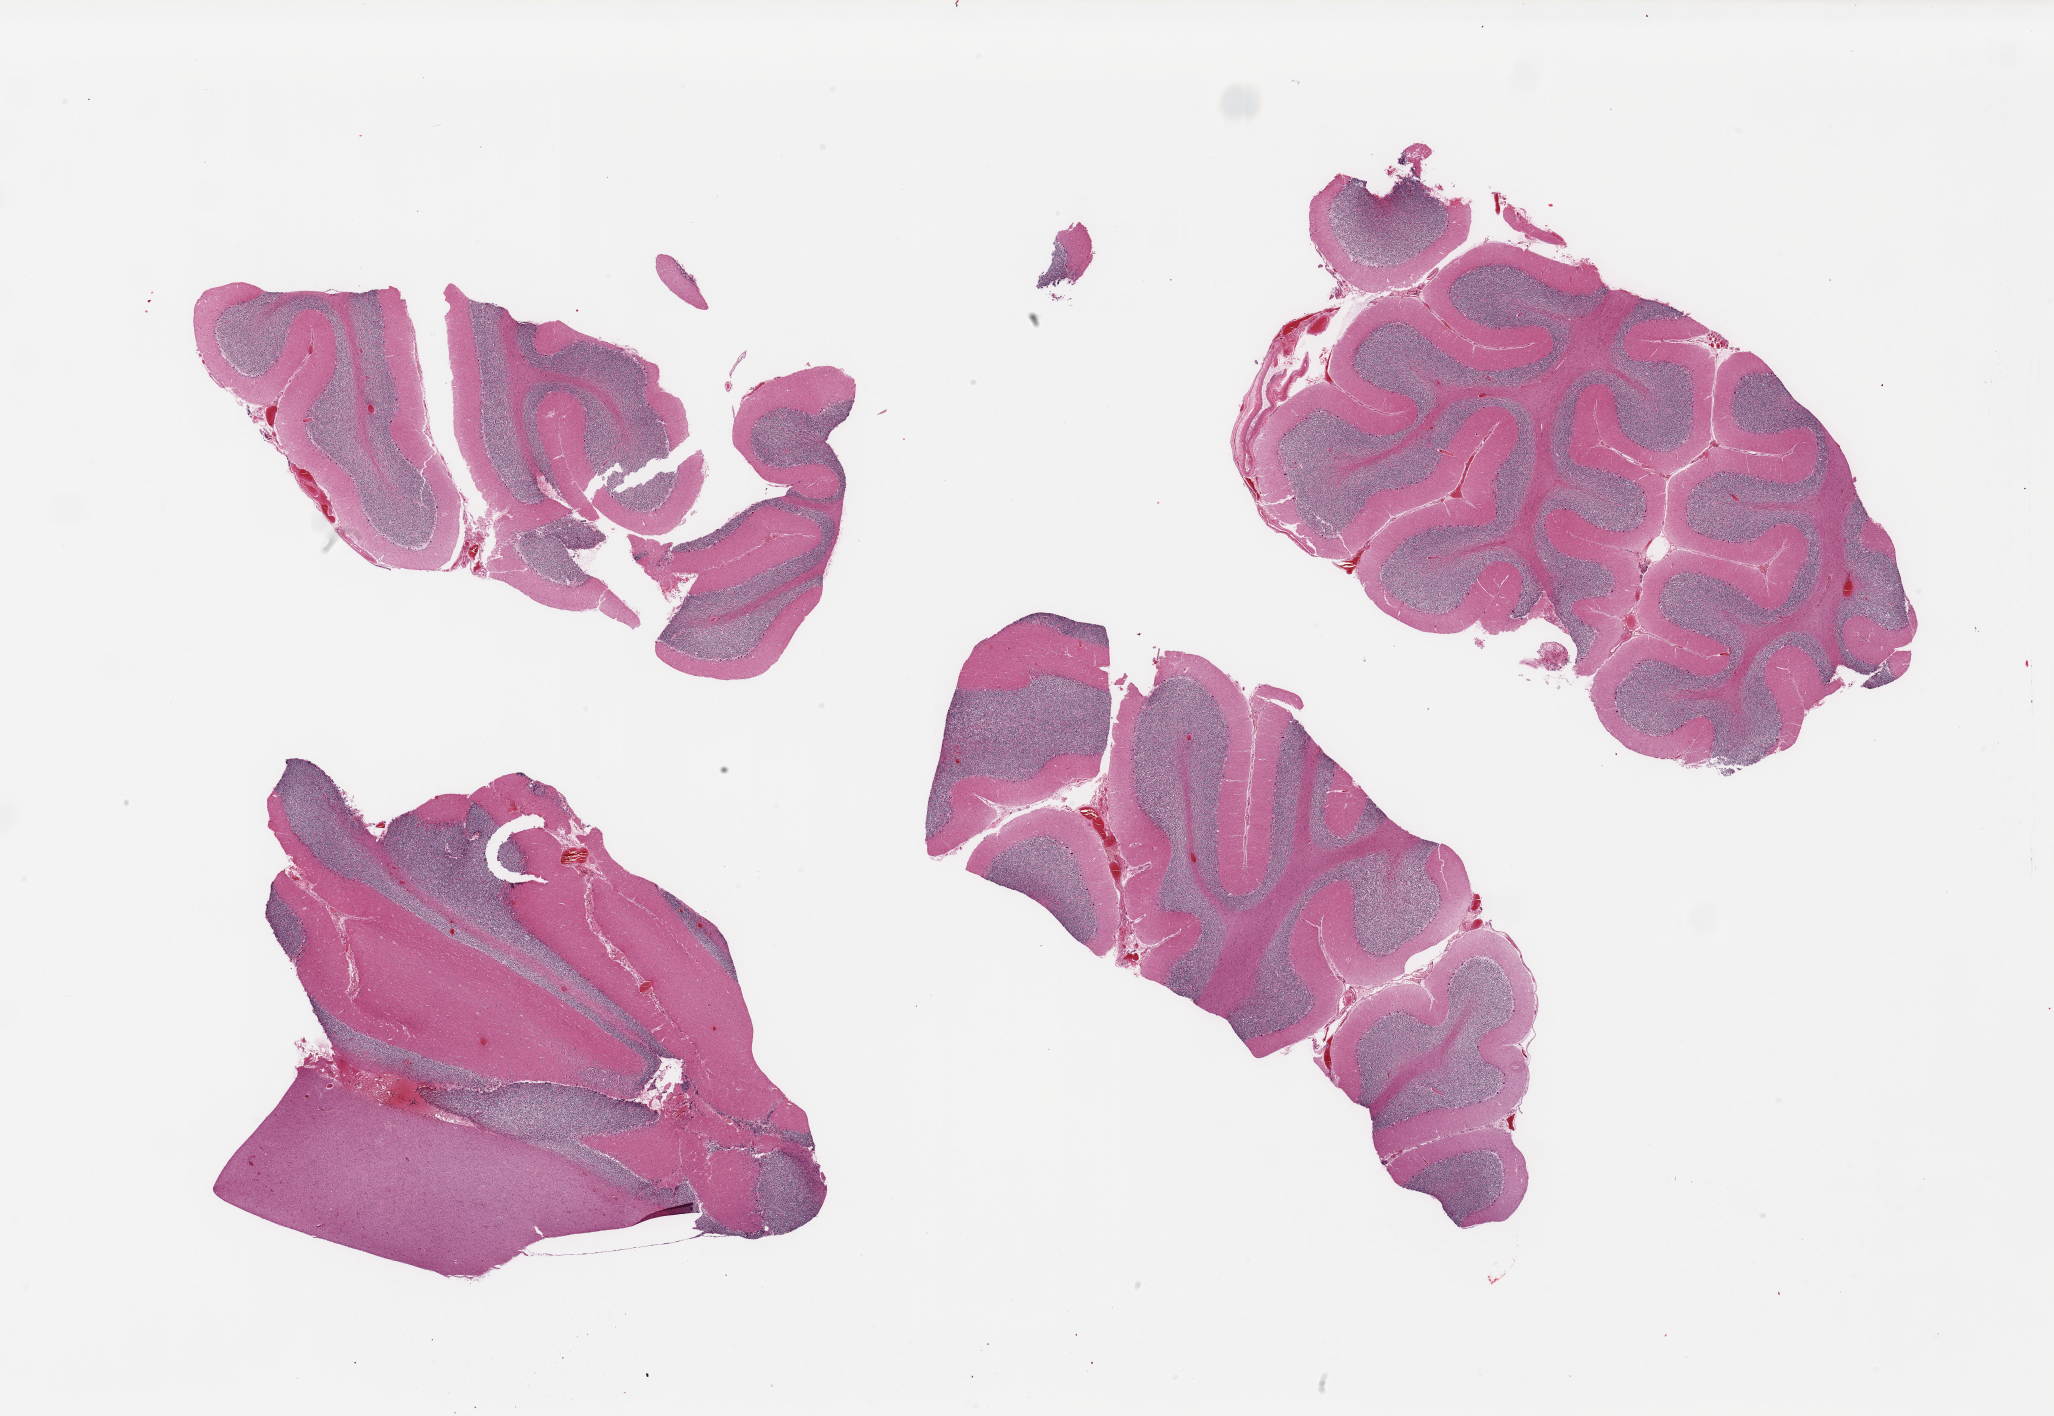
Hematoxylin and eosin (H&E) whole-slide image, whole scanned area (about 32.5 x 22.4 mm) shown as a low-resolution overview, PAXgene-fixed paraffin-embedded (PFPE) section, target tissue: cerebellum, donor tissue sample. Donor: female.
* reviewer comment on this tissue sample: 4 partially fragmented pieces